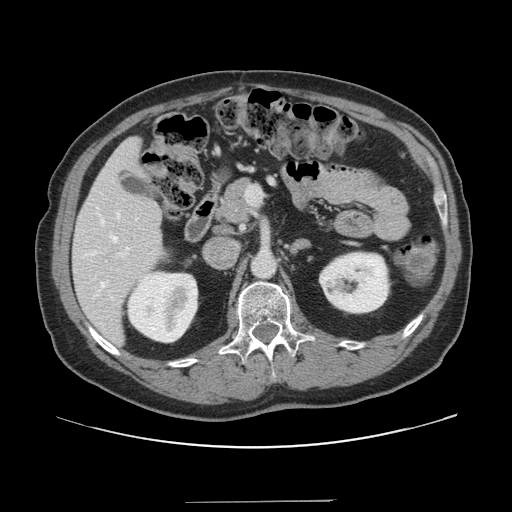
Contrast-enhanced abdominal CT, one axial slice. Slice 74 of 151 in the series (ordered by position). Intravenous contrast given. Soft-tissue window (W 400 / L 40 HU). 2.5 mm slice thickness. 512 × 512 image matrix, field of view 399 × 399 mm. Male patient, age 63 years. Case-level facts recorded for this patient, not image findings: diagnosis: colorectal cancer liver metastases, imaged before liver resection; multiple liver metastases: no; largest metastasis: 2.1 cm.
Structures marked on this image (manually delineated by an expert):
- hepatic veins: box from (x=100, y=212) to (x=120, y=288) px
- liver: (x=73, y=139)–(x=164, y=345)
- planned liver remnant (the part of the liver to remain after resection): (x=73, y=139)–(x=164, y=345)
- portal vein (with intrahepatic branches): (x=117, y=188)–(x=261, y=258)